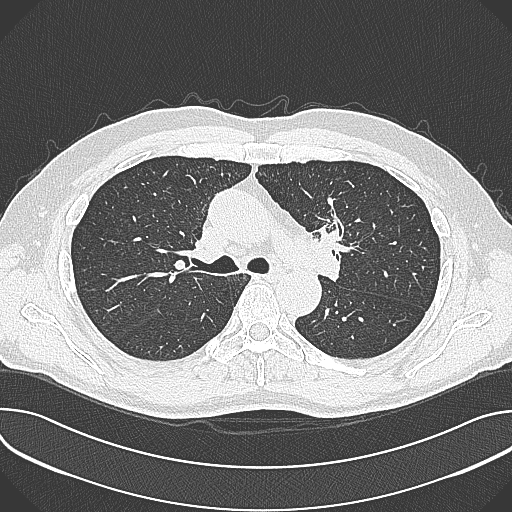
Axial slice from a low-dose chest CT screening exam; baseline annual screen; lung window (W 1500 / L -600 HU); 512 × 512 image matrix, field of view 380 × 380 mm. Male, age 59 years at enrolment. Current smoker at enrolment.
Expert-annotated lung lesion, bounding box <303,193,365,257> (left, top, right, bottom; pixels). The screening reader recorded 2 non-calcified nodules or masses ≥4 mm on this exam; which of them this box marks is not recorded. Official screen result: positive, change unspecified: nodule(s) >= 4 mm or enlarging nodule(s), mass(es), or other non-specific abnormalities suspicious for lung cancer. Lung cancer was diagnosed 21 days after this screen: non-small cell carcinoma, left upper lobe, poorly differentiated (G3), stage IIIA (AJCC 6th edition), 35 mm at pathology.